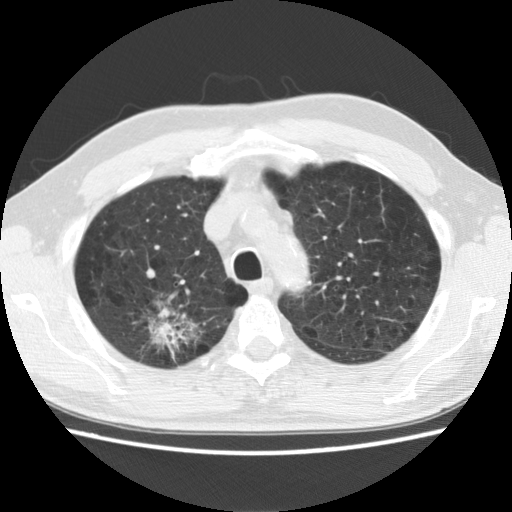
Chest CT (low-dose screening protocol), one axial image, baseline screening round, lung window (W 1500 / L -600 HU), 2.5 mm slice thickness, 120 kVp, slice 37 of 142 in the series. Male, age 64 years at enrolment.
• Expert reader's lesion annotation, bounding box <116,295,206,366> (left, top, right, bottom; pixels).
• Reader record for this screening exam (exam-level; its link to the box is not recorded): non-calcified nodule or mass ≥4 mm, right upper lobe, 39 × 31 mm, spiculated (stellate) margins, mixed attenuation.
• Official screen result: positive, change unspecified: nodule(s) >= 4 mm or enlarging nodule(s), mass(es), or other non-specific abnormalities suspicious for lung cancer.
• Lung cancer was diagnosed 74 days after this screen: adenocarcinoma, NOS, right upper lobe, moderately differentiated (G2), stage IB (AJCC 6th edition), 40 mm at pathology.